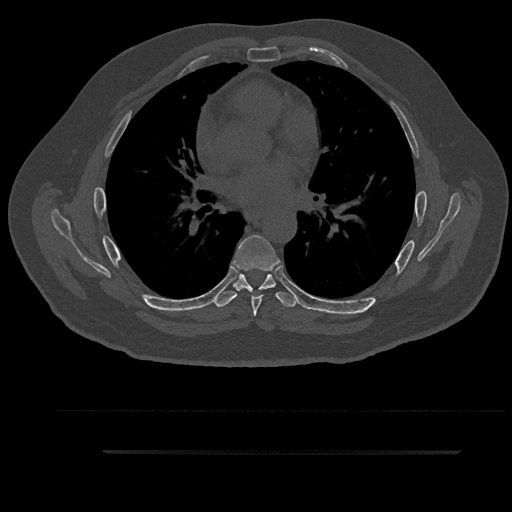
CT including the spine, one axial slice; slice 555 of 797 in the series (ordered by position); 120 kVp; bone window (W 1800 / L 400 HU); 0.5 mm slice thickness; 512 × 512 image matrix, field of view 432 × 432 mm. Patient: male, 63 years. Case-level facts recorded for this patient, not image findings: primary cancer: renal; vertebrae with lytic lesions (as recorded): T8.
Structures marked on this image (semi-automatic segmentation, software-assisted and operator-edited):
- T5 vertebra: bounding box [x1, y1, x2, y2] px = [260, 286, 266, 289]
- T6 vertebra: [233, 235, 280, 316]
- T7 vertebra: [214, 274, 298, 307]